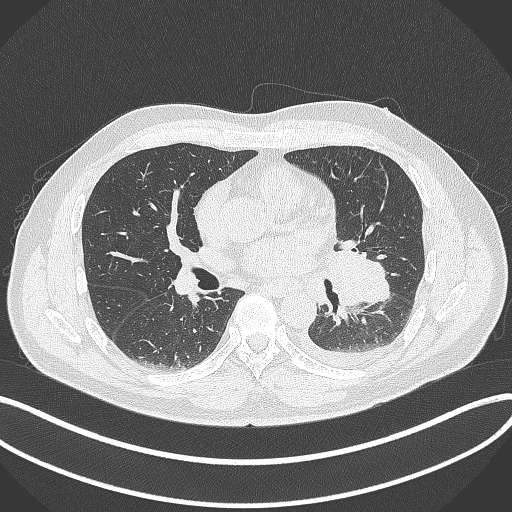
Chest CT, one axial slice; slice 185 of 342 in the series (ordered by position); lung window (W 1500 / L -600 HU); 512 × 512 image matrix, field of view 400 × 400 mm. Patient: male, 58 years. Case-level facts recorded for this patient, not image findings: clinical TNM (as recorded): T3 N1 M1b; histopathological grade: G3.
Annotated regions visible in this slice (rectangle marked by the reading radiologist):
- lung tumour (recorded histology: small cell carcinoma): bounding box (x1, y1, x2, y2) in pixels: (325, 233, 394, 313)